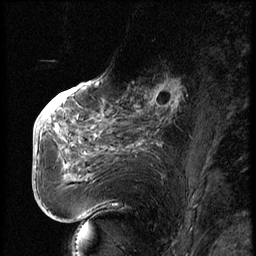
Breast MRI (dynamic contrast-enhanced), one sagittal slice; slice 29 of 74 in the series (ordered by position); dynamic contrast-enhanced series, image 2 of 3 at this slice position (ordered by acquisition); 1.5 T; TE 4.2 ms, TR 9 ms; 2.5 mm slice thickness; 256 × 256 image matrix, field of view 180 × 180 mm. Patient: female, 56 years. Case-level facts recorded for this patient, not image findings: setting: breast cancer imaged before/during neoadjuvant chemotherapy.
Annotated regions visible in this slice (semi-automatic segmentation, software-assisted and operator-edited):
- analysis volume of interest (the breast-tissue region the enhancement analysis was run in; not a lesion): bounding box (x1, y1, x2, y2) in pixels: (123, 71, 195, 131)
- tumour enhancement mask (voxels above the 140 % enhancement threshold inside the analysis volume of interest): (152, 79, 182, 113)